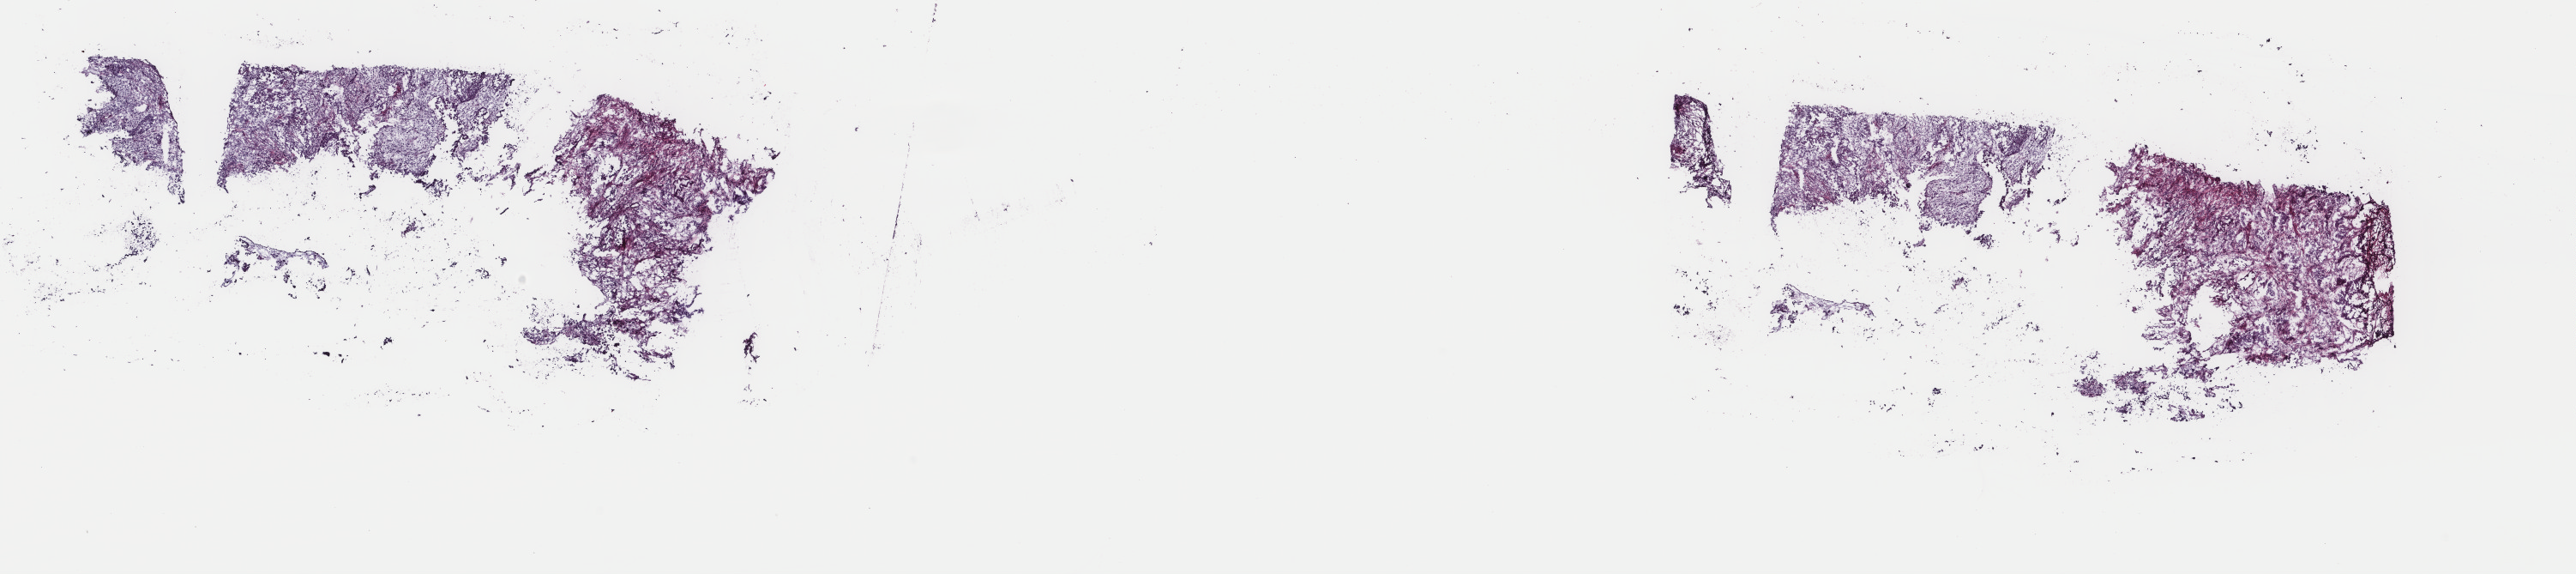
Whole-slide histology image, H&E — low-resolution overview of the scanned area, about 23.8 x 5.3 mm (slide scanned at 40x). Frozen section. Primary tumour sample from the uterus. Patient: female, age at initial diagnosis 77 years. Slide review estimates, as recorded: tumour cells 90%, tumour nuclei 90%, normal cells 0%, stromal cells 5%, necrosis 5%. Infiltration values recorded for this section: lymphocyte infiltration 20%, monocyte infiltration 20%, neutrophil infiltration 40%.
FIGO stage: IVB. Diagnosis: Mullerian mixed tumor (endometrium).